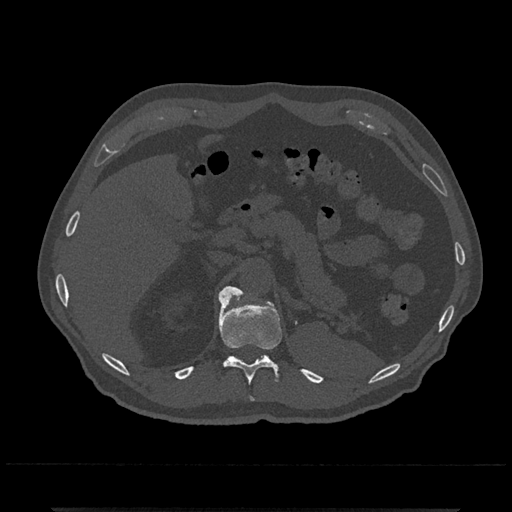
CT including the spine, one axial slice. Slice 481 of 797 in the series (ordered by position). Reconstruction kernel Br40s/3. Bone window (W 1800 / L 400 HU). 0.5 mm slice thickness. 512 × 512 image matrix, field of view 393 × 393 mm. Patient: male, 67 years. From the clinical record (not read from this slice): primary cancer: prostate.
Outlined on this slice (semi-automatic segmentation, software-assisted and operator-edited):
- T11 vertebra: box from (x=218, y=293) to (x=282, y=402) px
- T12 vertebra: (x=220, y=286)–(x=244, y=299)